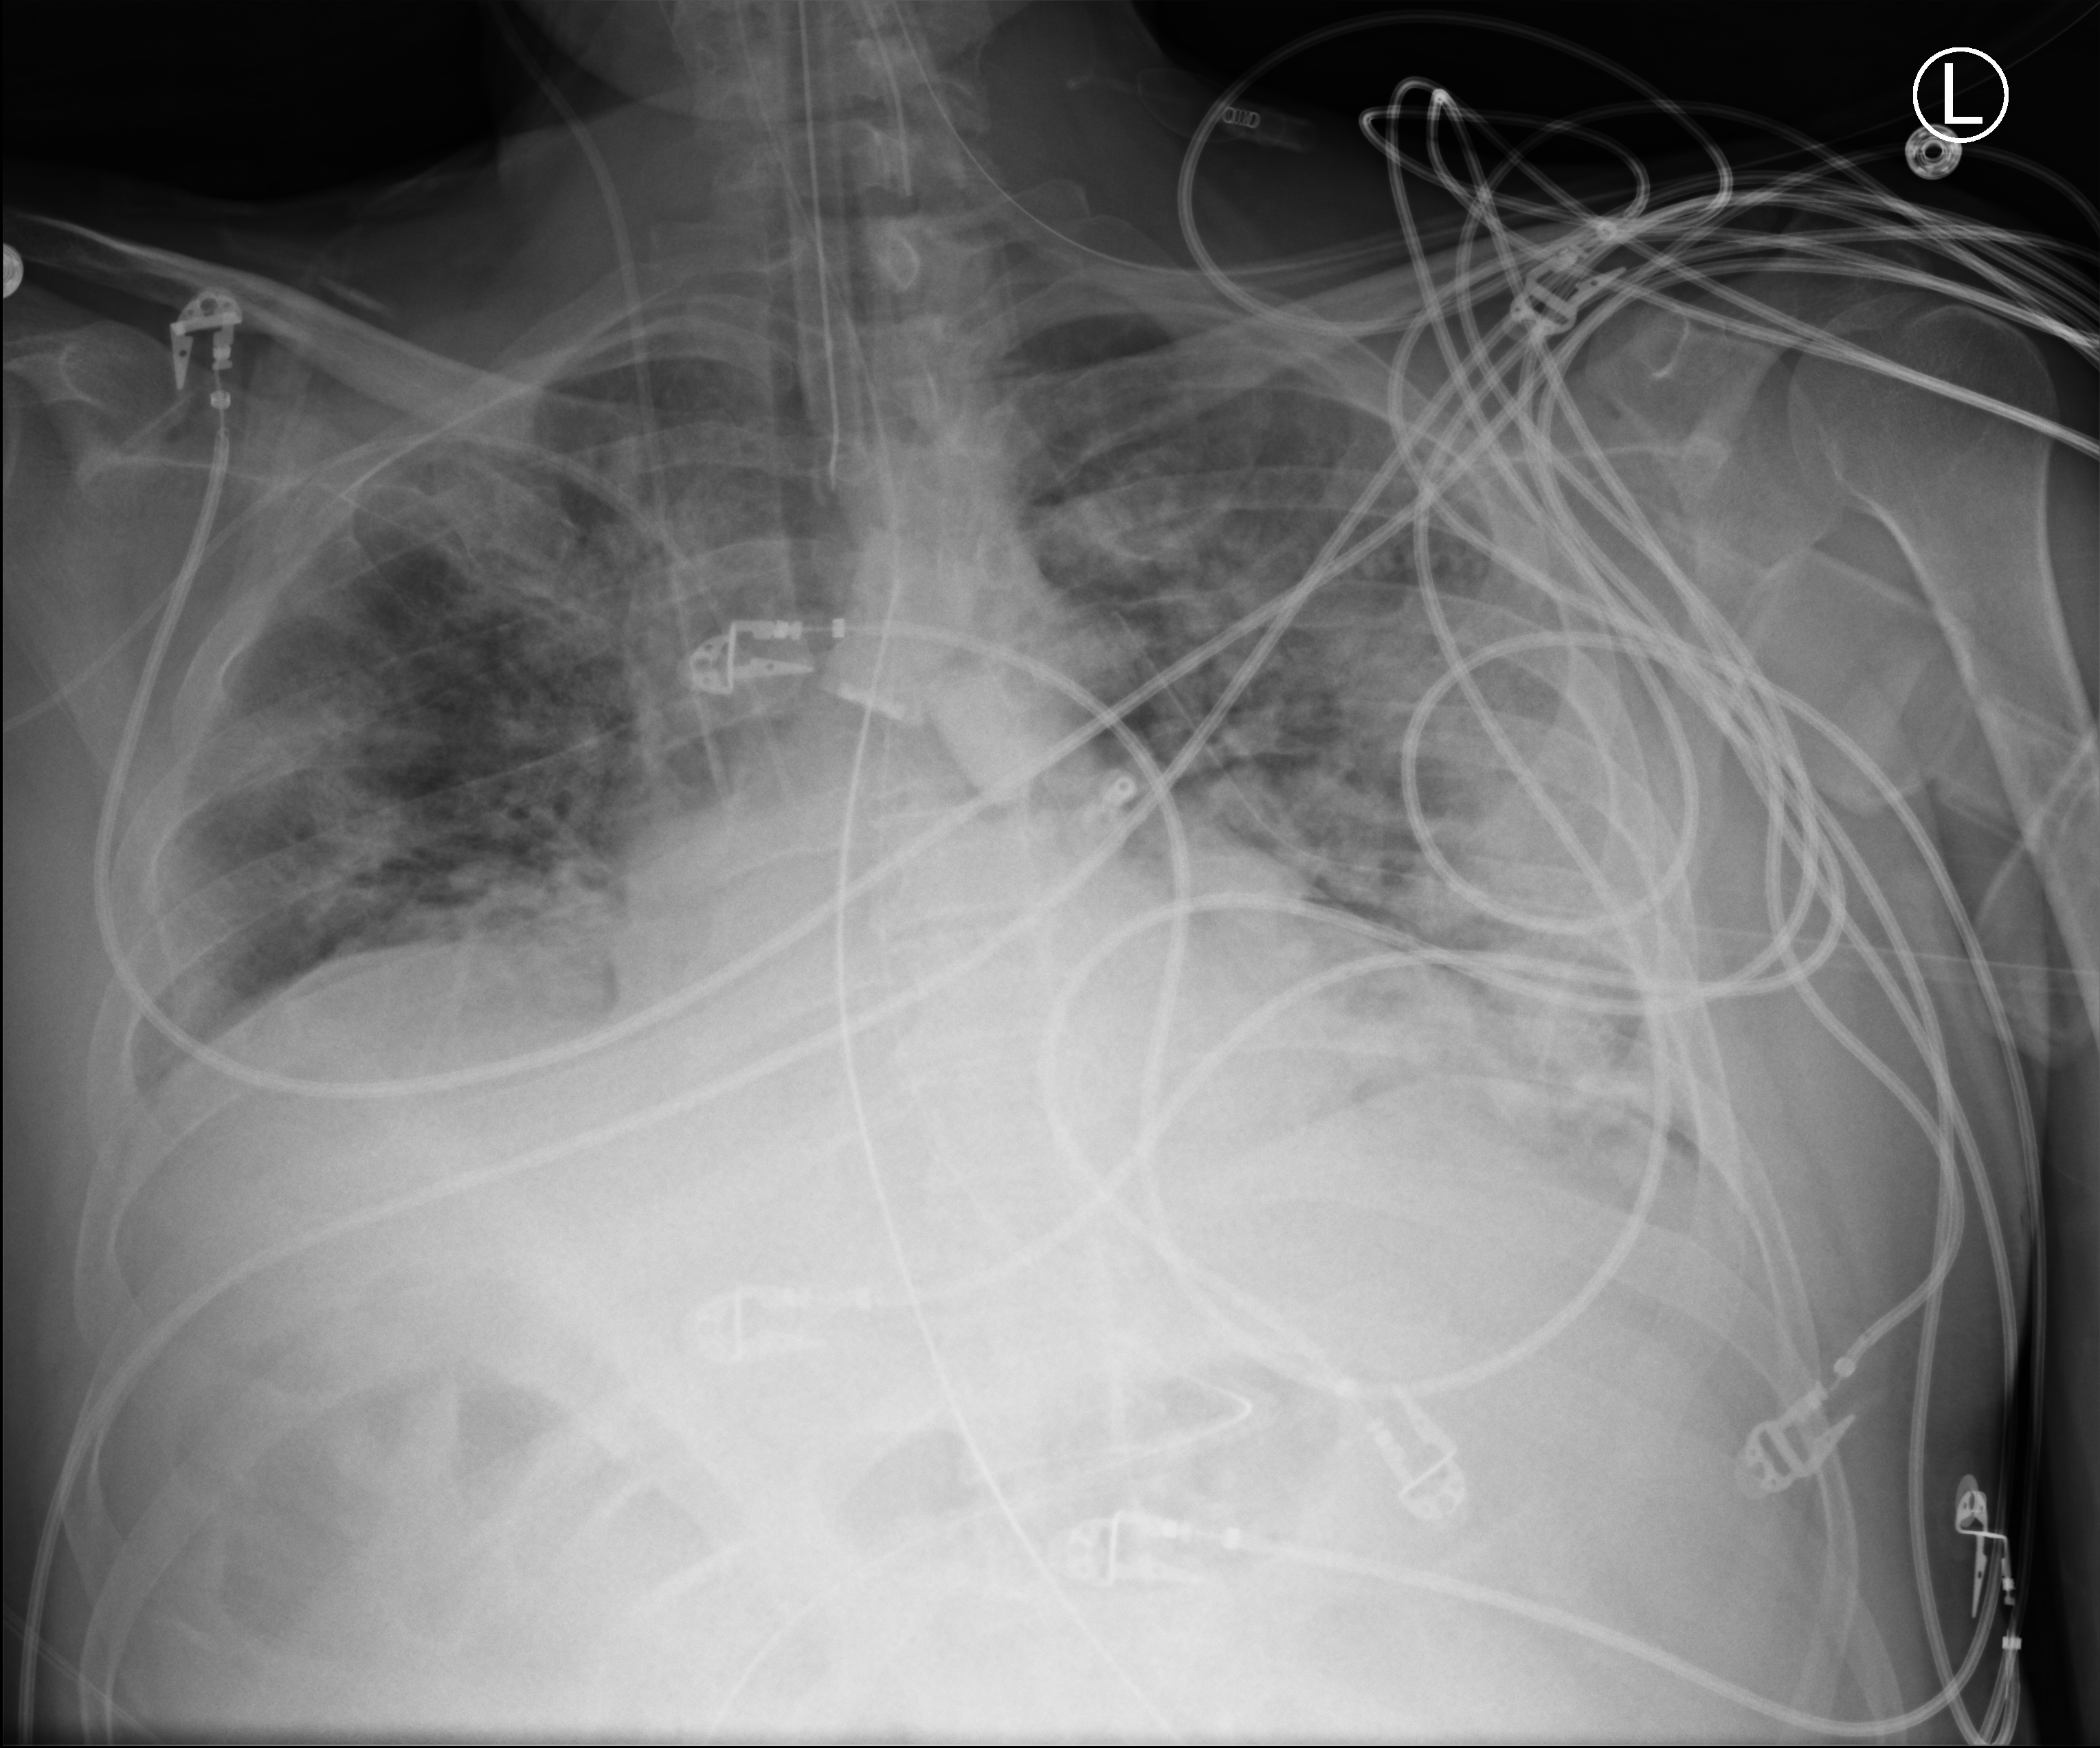
Bedside chest radiograph (computed radiography), anteroposterior (AP) projection. Male patient hospitalised with COVID-19, age 18–59 years.
From the hospital-stay record, not from the radiograph (when in the stay this image was taken is not recorded):
- mechanically ventilated during this hospital stay: yes